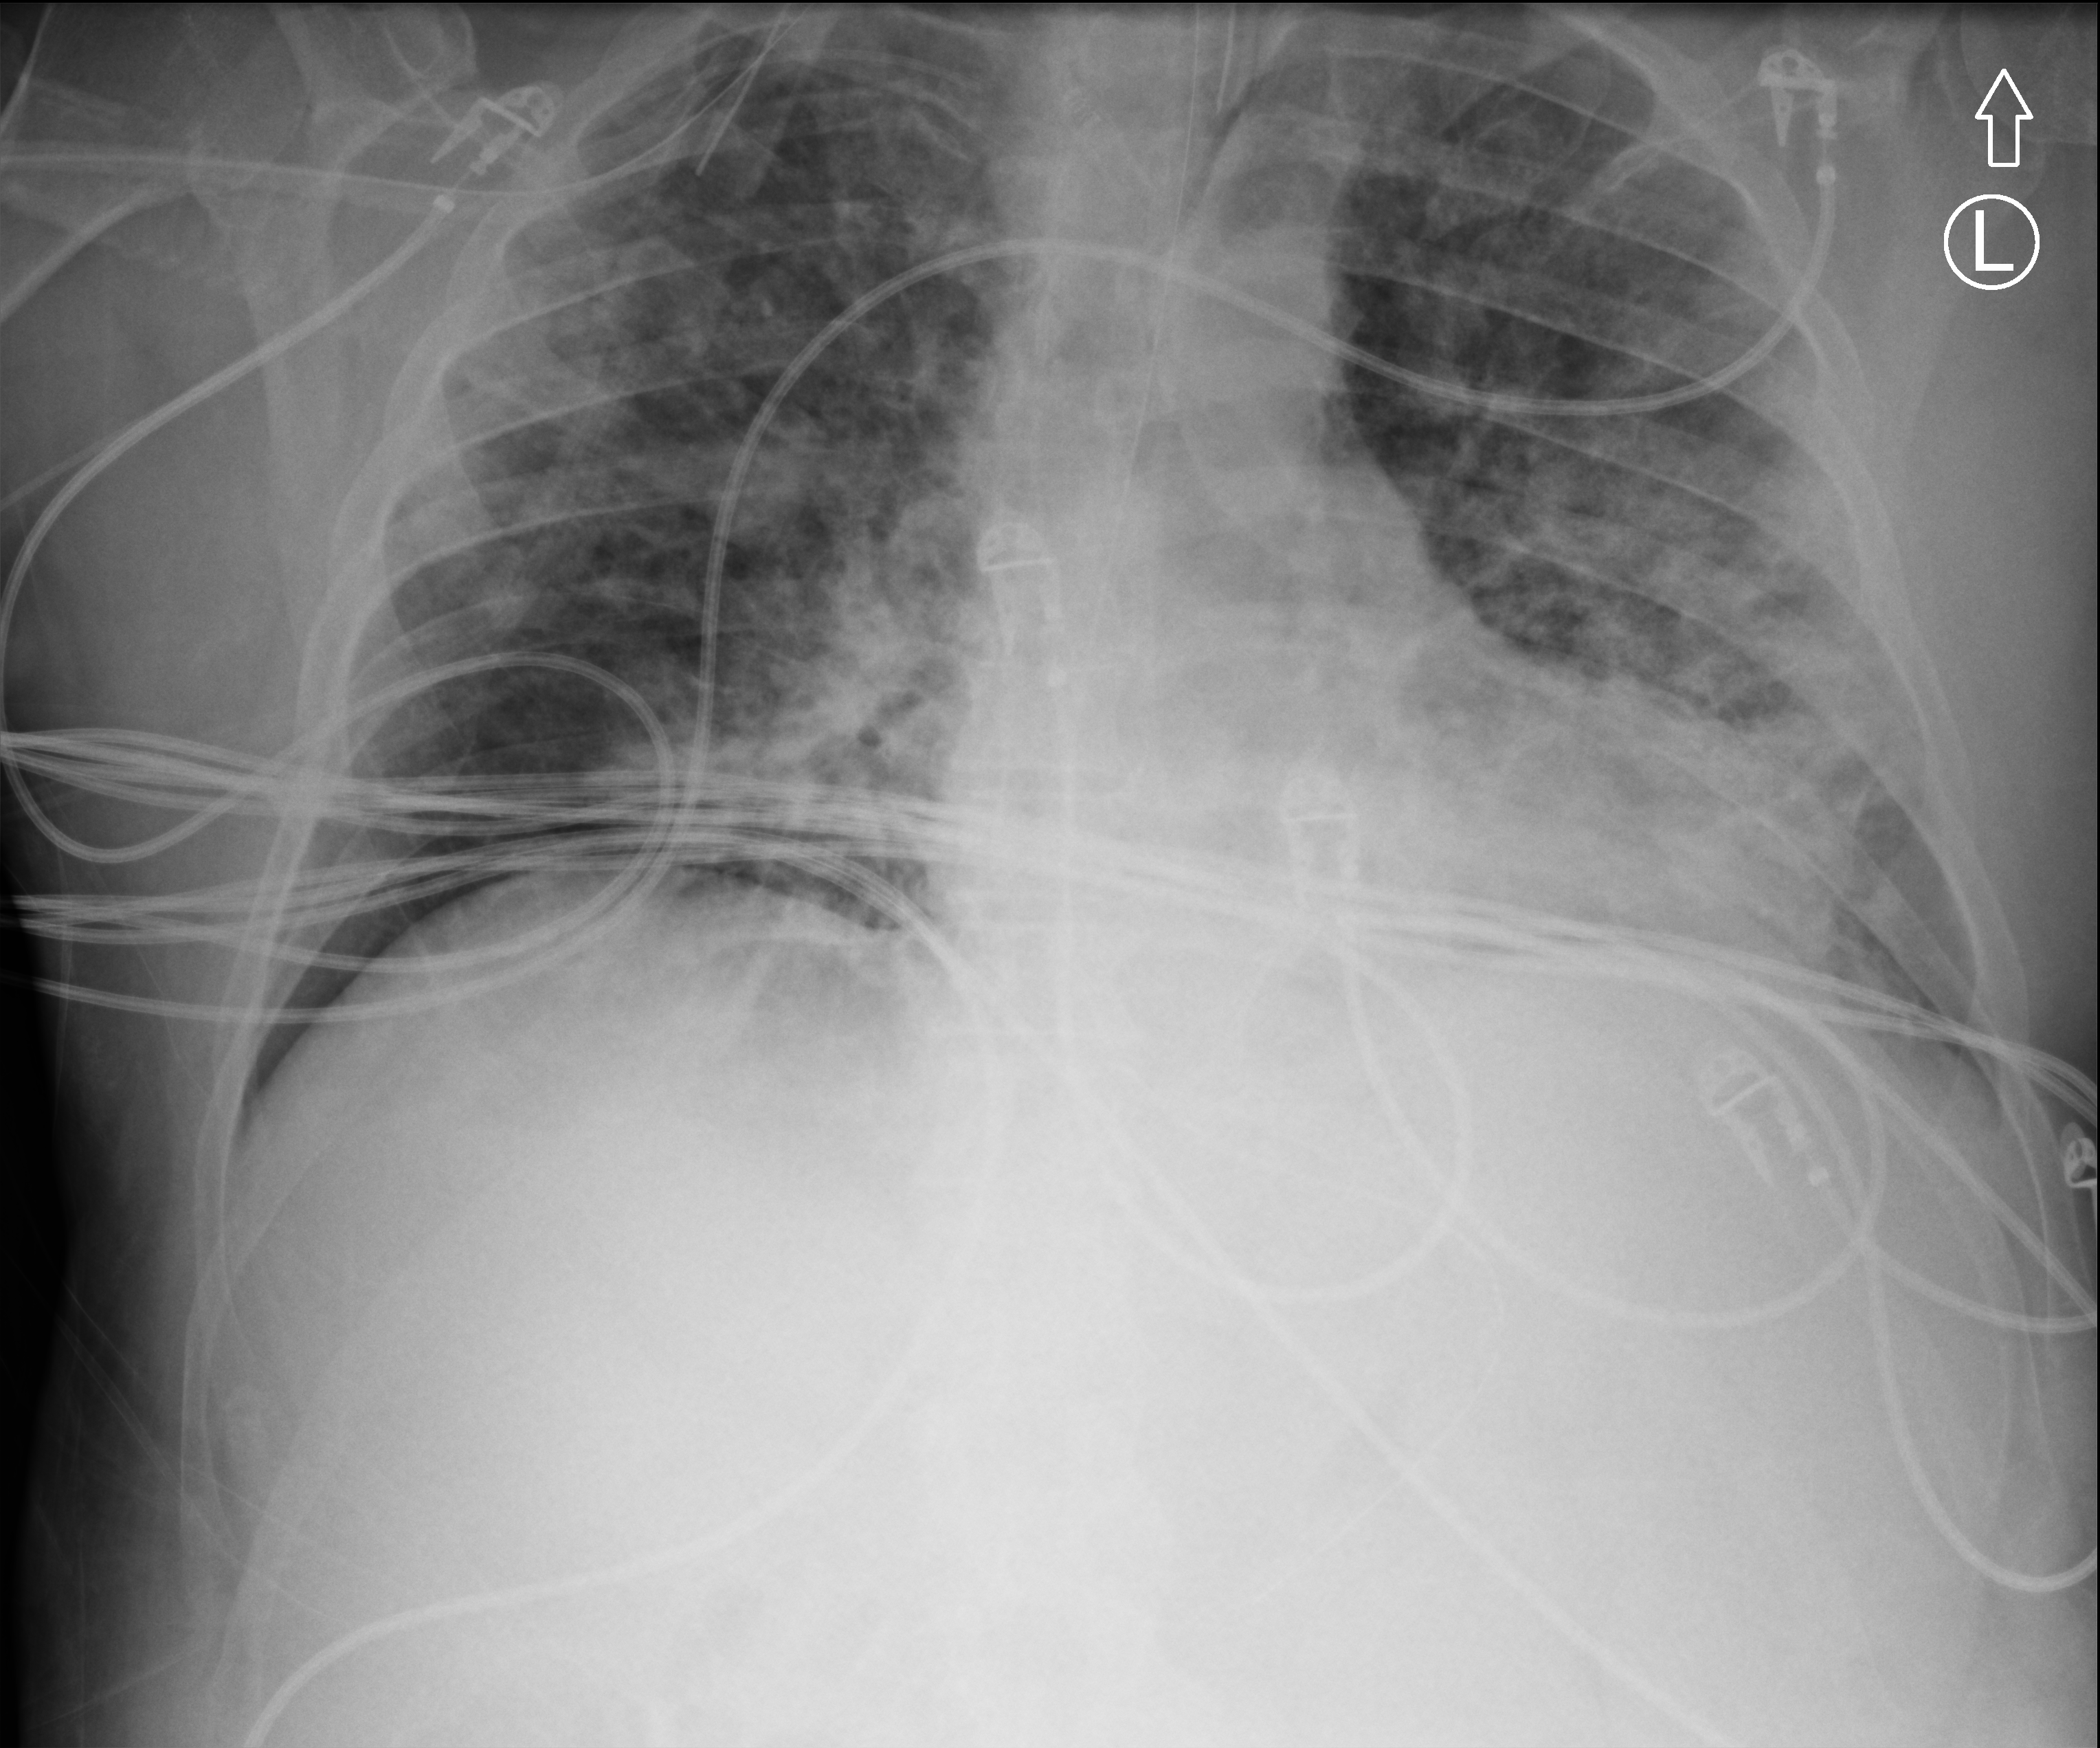
Bedside chest radiograph (computed radiography), anteroposterior (AP) projection. Patient hospitalised with COVID-19; male, aged 60–74 years.
From the hospital-stay record, not from the radiograph (when in the stay this image was taken is not recorded):
- COPD (admission record): no